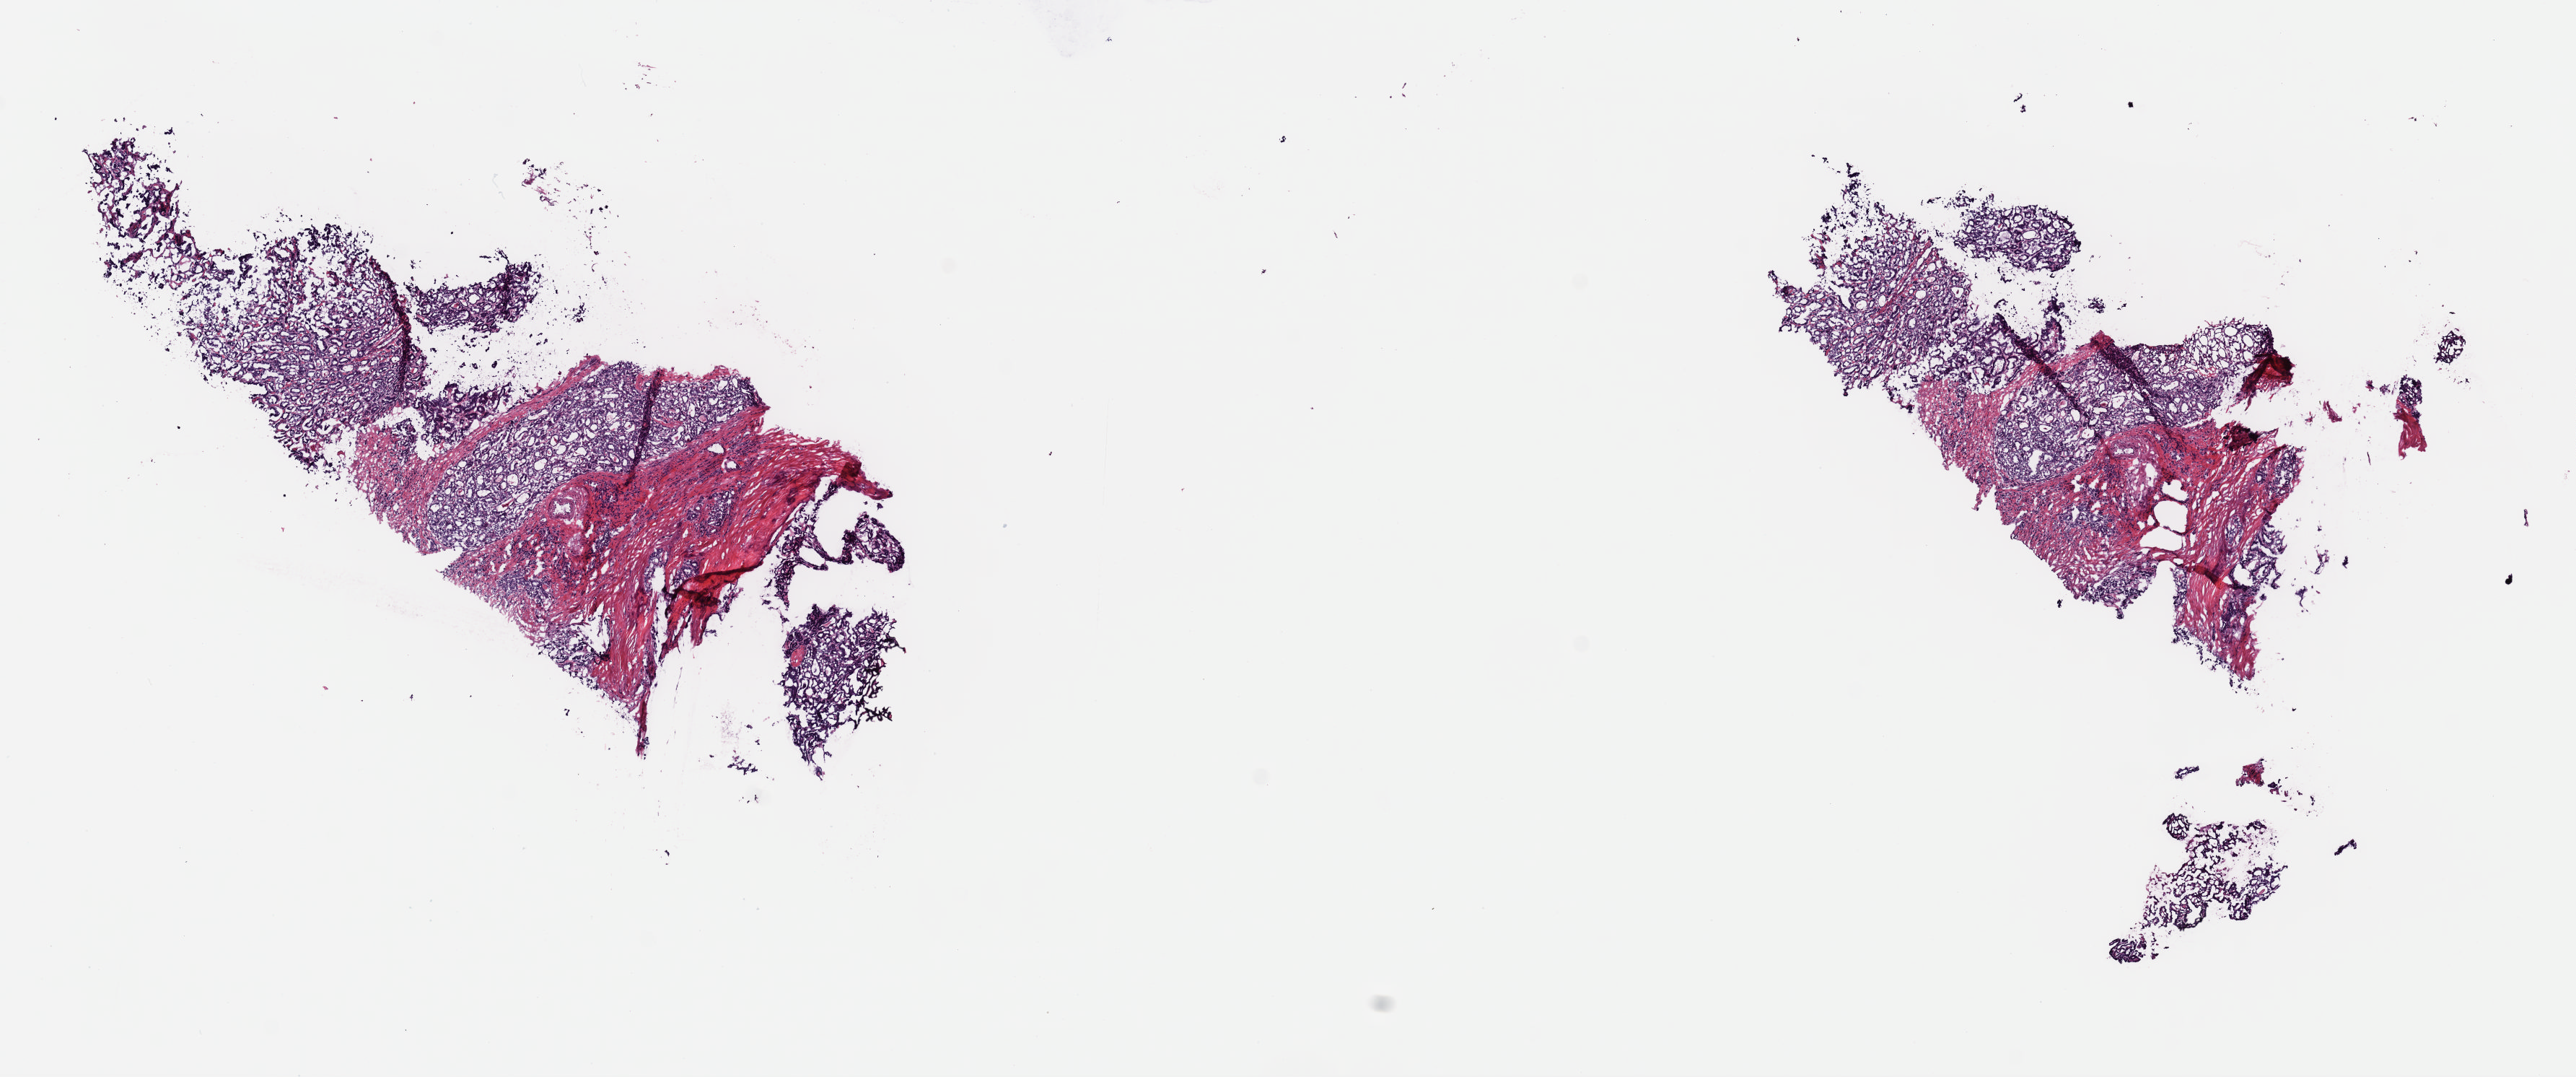
Digitized H&E-stained tissue section (whole slide) — shown as a low-resolution overview of the whole scanned area (about 14.1 x 5.9 mm). Frozen section from the top of the tissue portion. Thyroid, primary tumour sample. Male, age 51 years at initial diagnosis. Composition of this section per pathologist review: tumour cells 70%, tumour nuclei 90%, normal cells 0%, stromal cells 30%, necrosis 0%. Infiltration values recorded for this section: lymphocyte infiltration 1%, monocyte infiltration 1%, neutrophil infiltration 0%.
Lymph nodes positive (case pathology): 2 of 5 examined. AJCC pathologic stage: IVA (7th edition). Pathologic diagnosis: Papillary adenocarcinoma, NOS (thyroid gland).